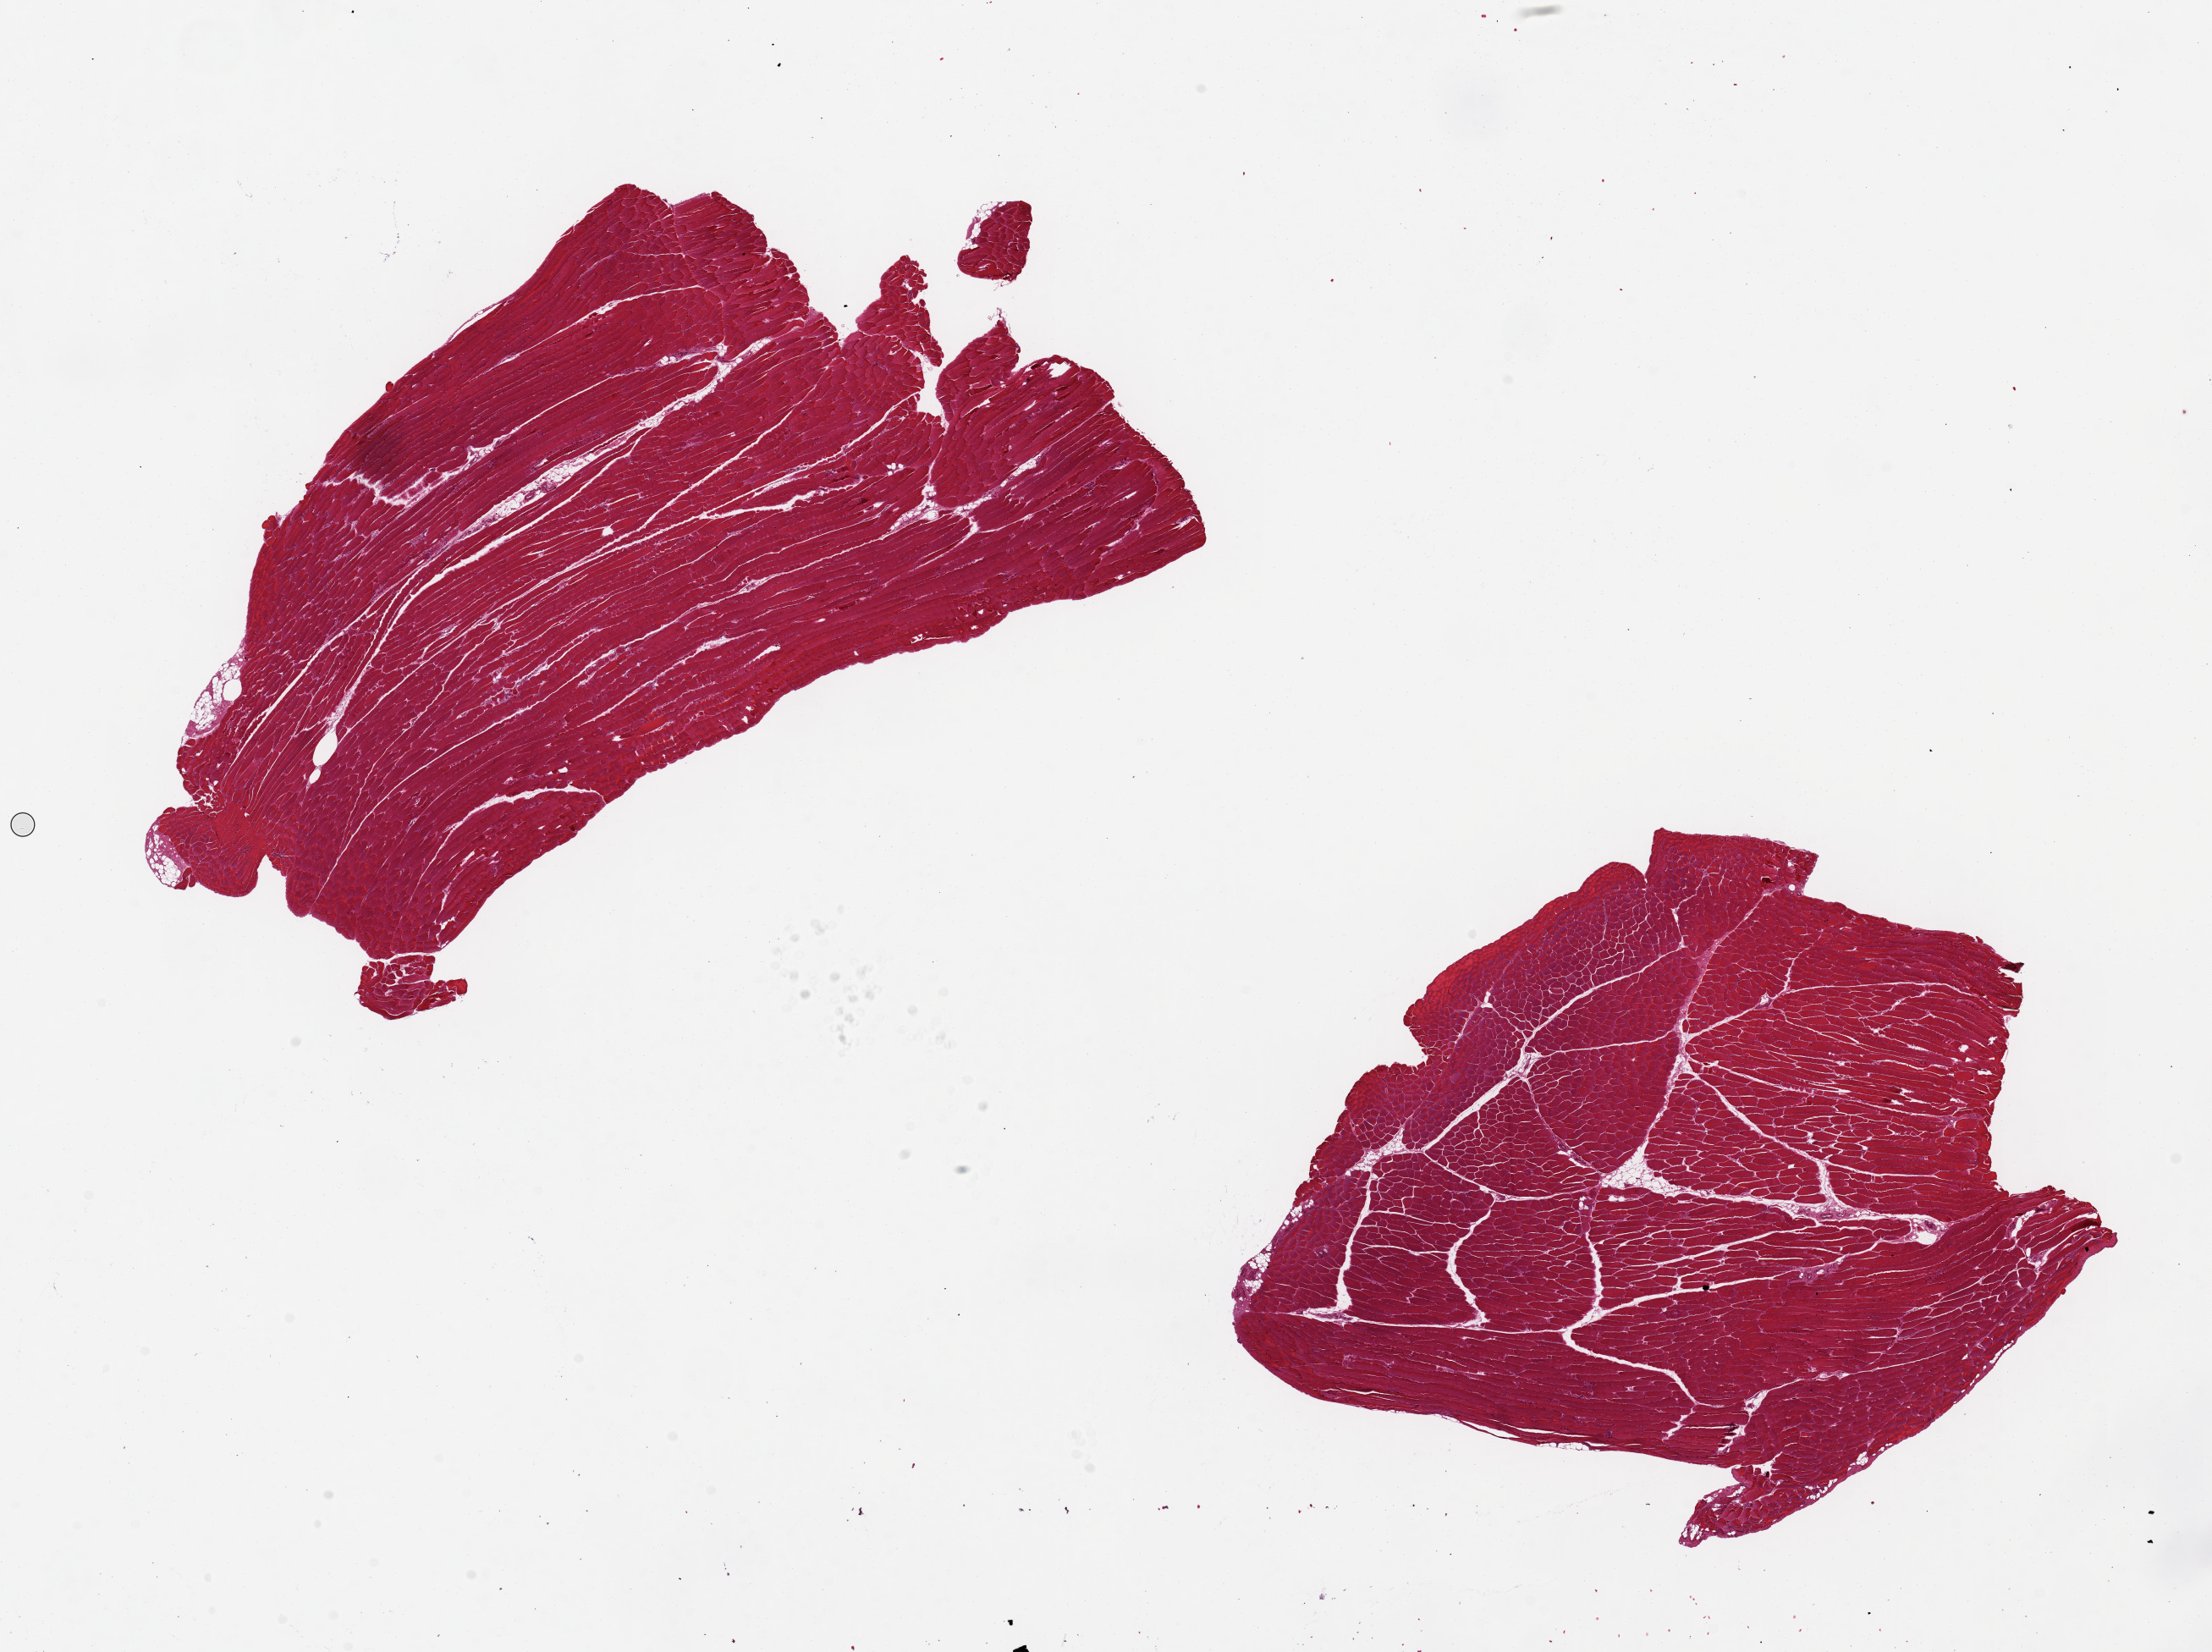
Hematoxylin and eosin (H&E) whole-slide image, brightfield — shown as a low-resolution overview of the whole scanned area (about 20.7 x 15.4 mm, from a 20x scan), PAXgene-fixed, paraffin-embedded tissue, section of skeletal muscle (target tissue), donor tissue sample. Donor sex: female.
Reviewer comment on this tissue sample: 2 pieces, ~7x7mm, minimal interstital fat.